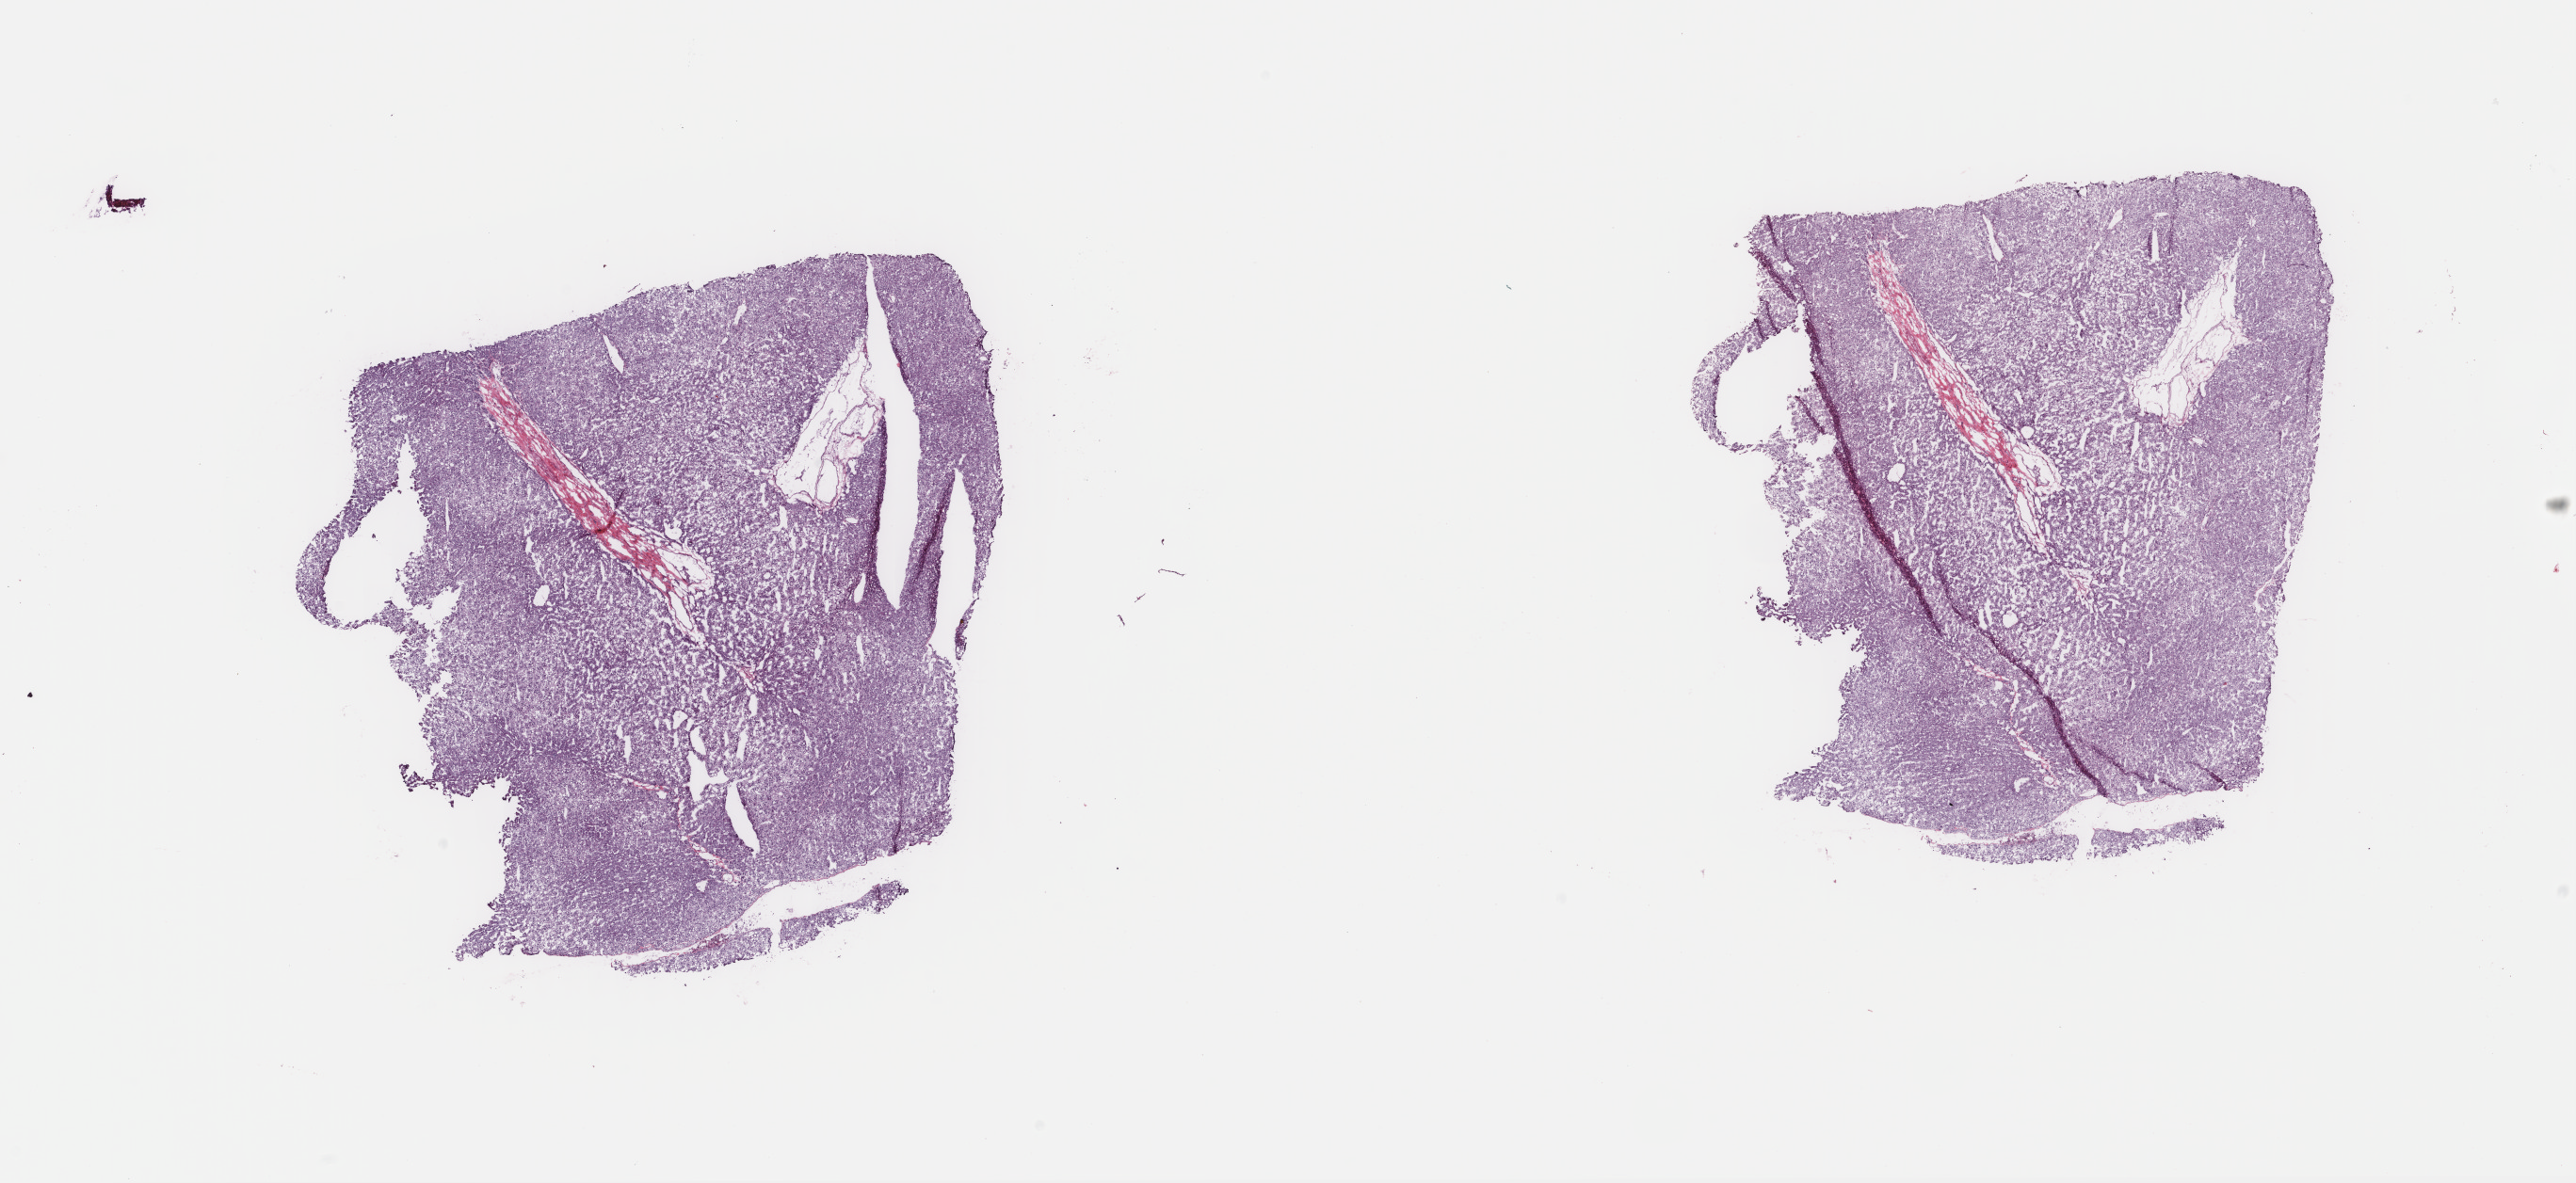
H&E-stained whole-slide image — whole scanned area (about 21.7 x 10.0 mm, from a 40x scan) shown as a low-resolution overview; frozen section from the top of the tissue portion; sample: primary tumour, liver. Patient: female, age at initial diagnosis 76 years. Histologic grade: G1 (well differentiated). Pathologist review of this section (percent, as recorded): tumour cells 95%, tumour nuclei 95%, normal cells 0%, stromal cells 5%, necrosis 0%. Inflammatory infiltration, as recorded: lymphocyte infiltration 1%, monocyte infiltration 0%, neutrophil infiltration 0%.
Pathologic diagnosis: Hepatocellular carcinoma, NOS. AJCC pathologic stage: I (5th edition).